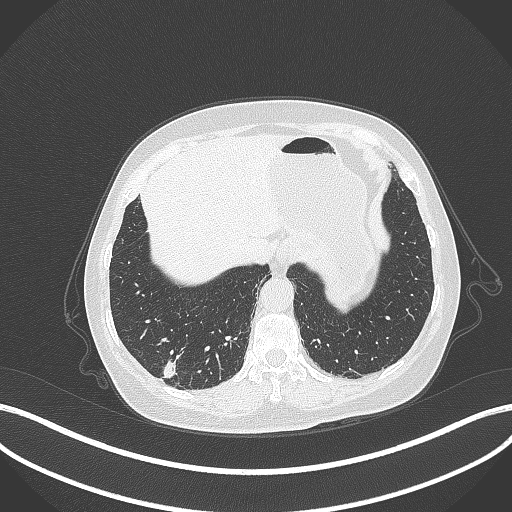
Chest CT, one axial slice; position 49 of 333 along the scan axis; lung window (W 1500 / L -600 HU); 1 mm slice thickness; 512 × 512 image matrix, field of view 400 × 400 mm. Patient: female, 69 years. Case-level facts recorded for this patient, not image findings: clinical TNM (as recorded): T1b N0 M0; histopathological grade: G2-3.
Structures marked on this image (rectangle marked by the reading radiologist):
- lung tumour (recorded histology: adenocarcinoma): bounding box <159,357,180,381> (left, top, right, bottom; pixels)